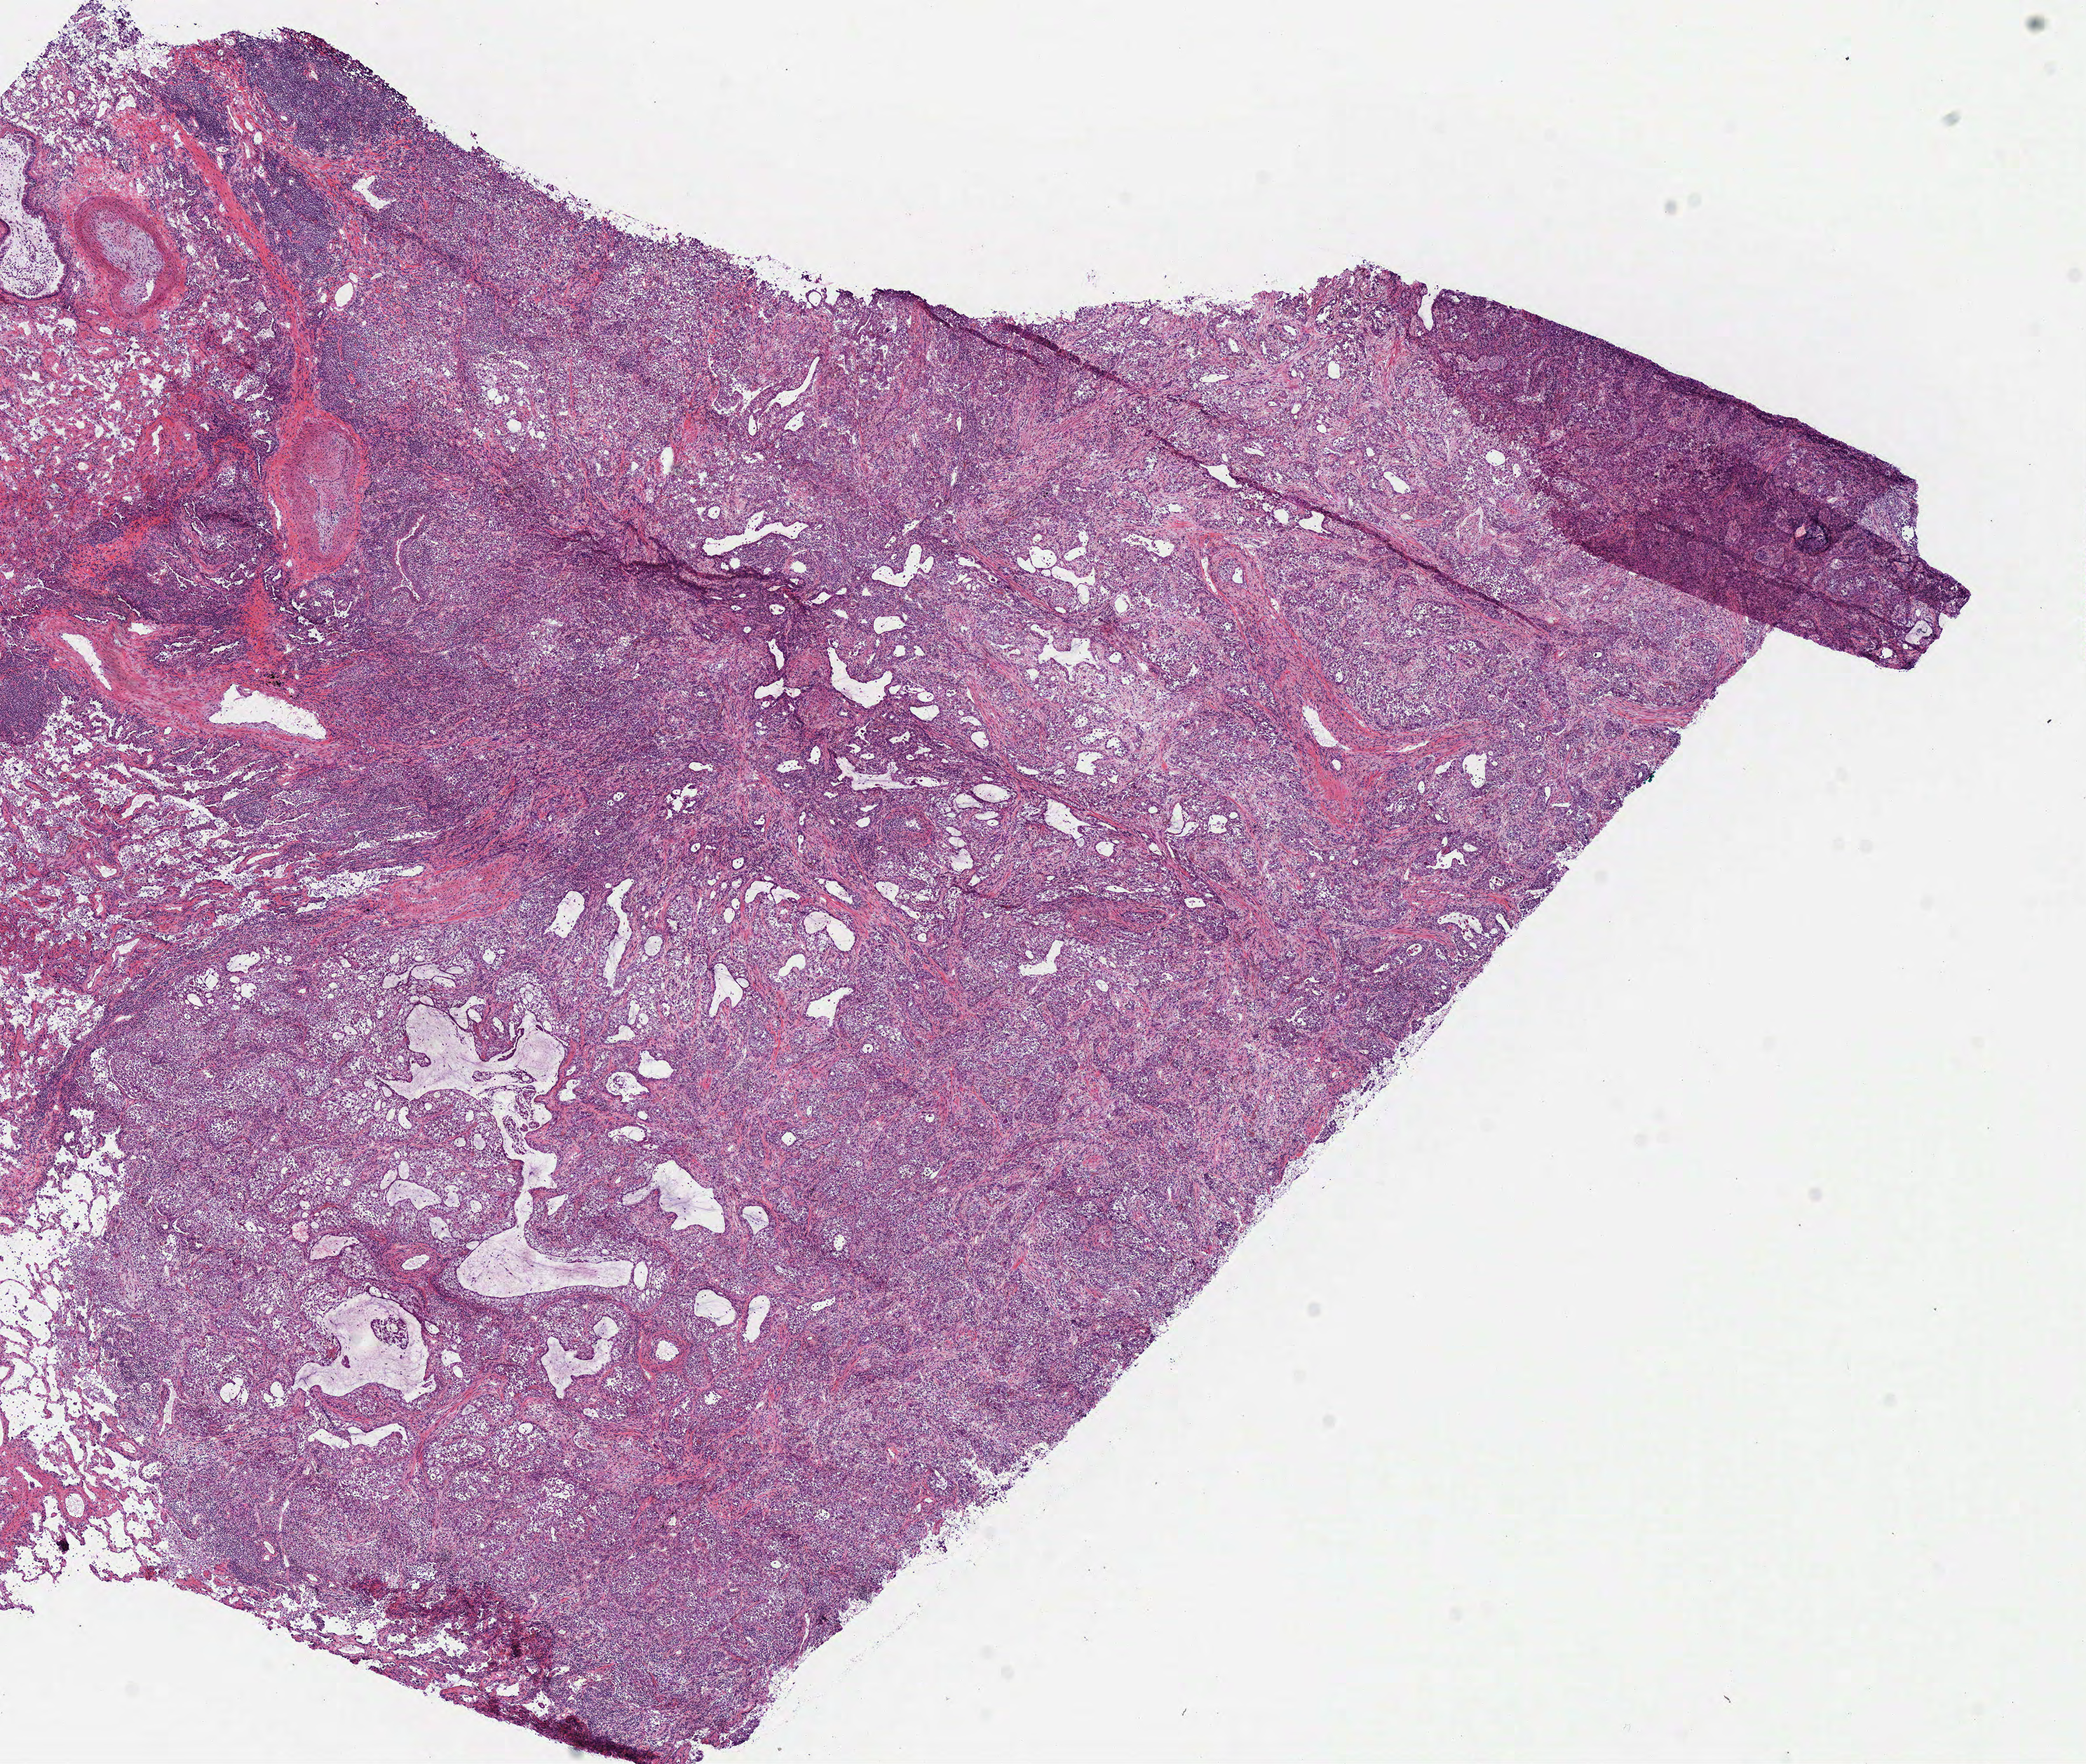
H&E-stained whole-slide image — a low-resolution overview of the entire scanned area, about 11.7 x 9.9 mm (from a 40x scan); frozen section from the bottom of the tissue portion; sample: primary tumour, lung. Patient: female, age at initial diagnosis 62 years. Slide review estimates, as recorded: tumour cells 80%, tumour nuclei 60%, normal cells 20%, stromal cells 0%, necrosis 0%. Infiltration values recorded for this section: lymphocyte infiltration 25%, monocyte infiltration 0%, neutrophil infiltration 5%.
- laterality: right
- diagnosis: Adenocarcinoma, NOS (upper lobe, lung)
- AJCC pathologic stage: IA (7th edition)